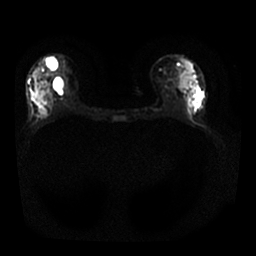
Breast MRI, one axial slice. Diffusion-weighted series; image 2 of 4 stored at this slice position (different b-values; order by instance number). 1.5 T. 256 × 256 image matrix, field of view 330 × 330 mm. Female patient.
Structures marked on this image (expert manual segmentation):
- tumour on diffusion-weighted imaging: bounding box <37,95,54,121> (left, top, right, bottom; pixels)